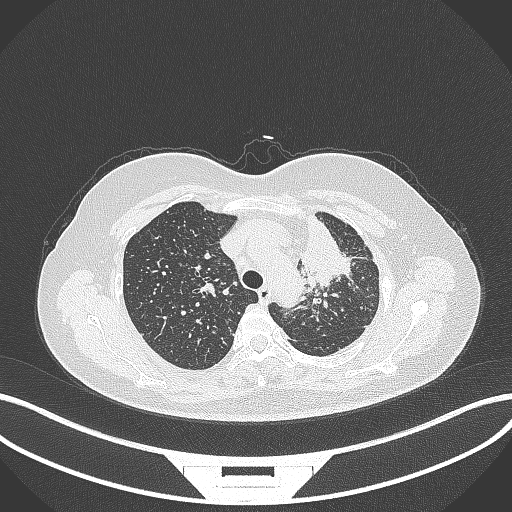
Chest CT, one axial slice. Slice 255 of 348 in the series (ordered by position). Reconstruction kernel B70f. Lung window (W 1500 / L -600 HU). 1 mm slice thickness. 512 × 512 image matrix. Female patient, age 49 years. Case-level facts recorded for this patient, not image findings: clinical TNM (as recorded): T1c N0 M1.
Annotated regions visible in this slice (bounding box drawn by a radiologist):
- lung tumour (recorded histology: adenocarcinoma): bounding box (x1, y1, x2, y2) in pixels: (294, 208, 354, 285)